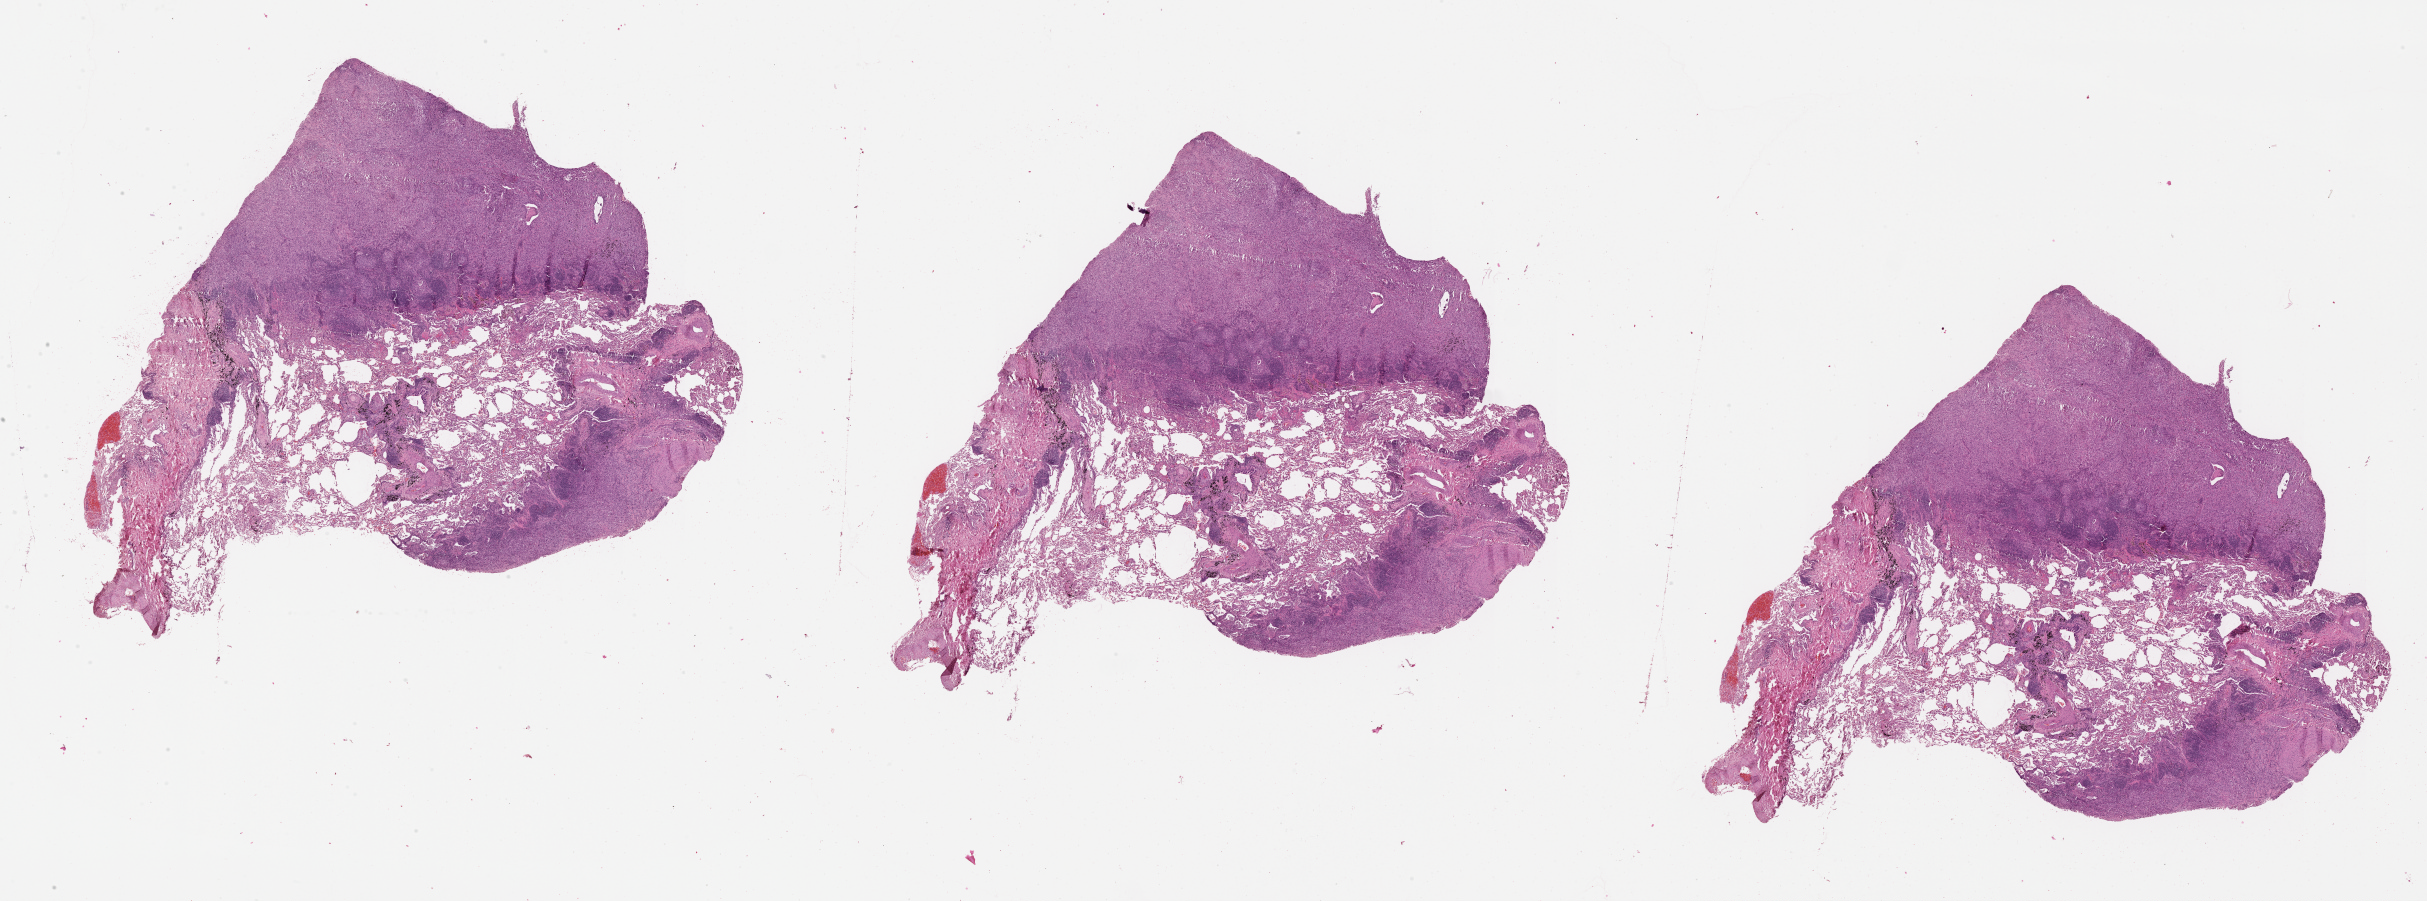
H&E whole-slide image, a low-resolution overview of the entire scanned area, about 39.1 x 14.5 mm (slide scanned at 20x); lung, tumour tissue. 77-year-old male patient.
Patient diagnosis (cohort enrolment): squamous cell carcinoma (lung).